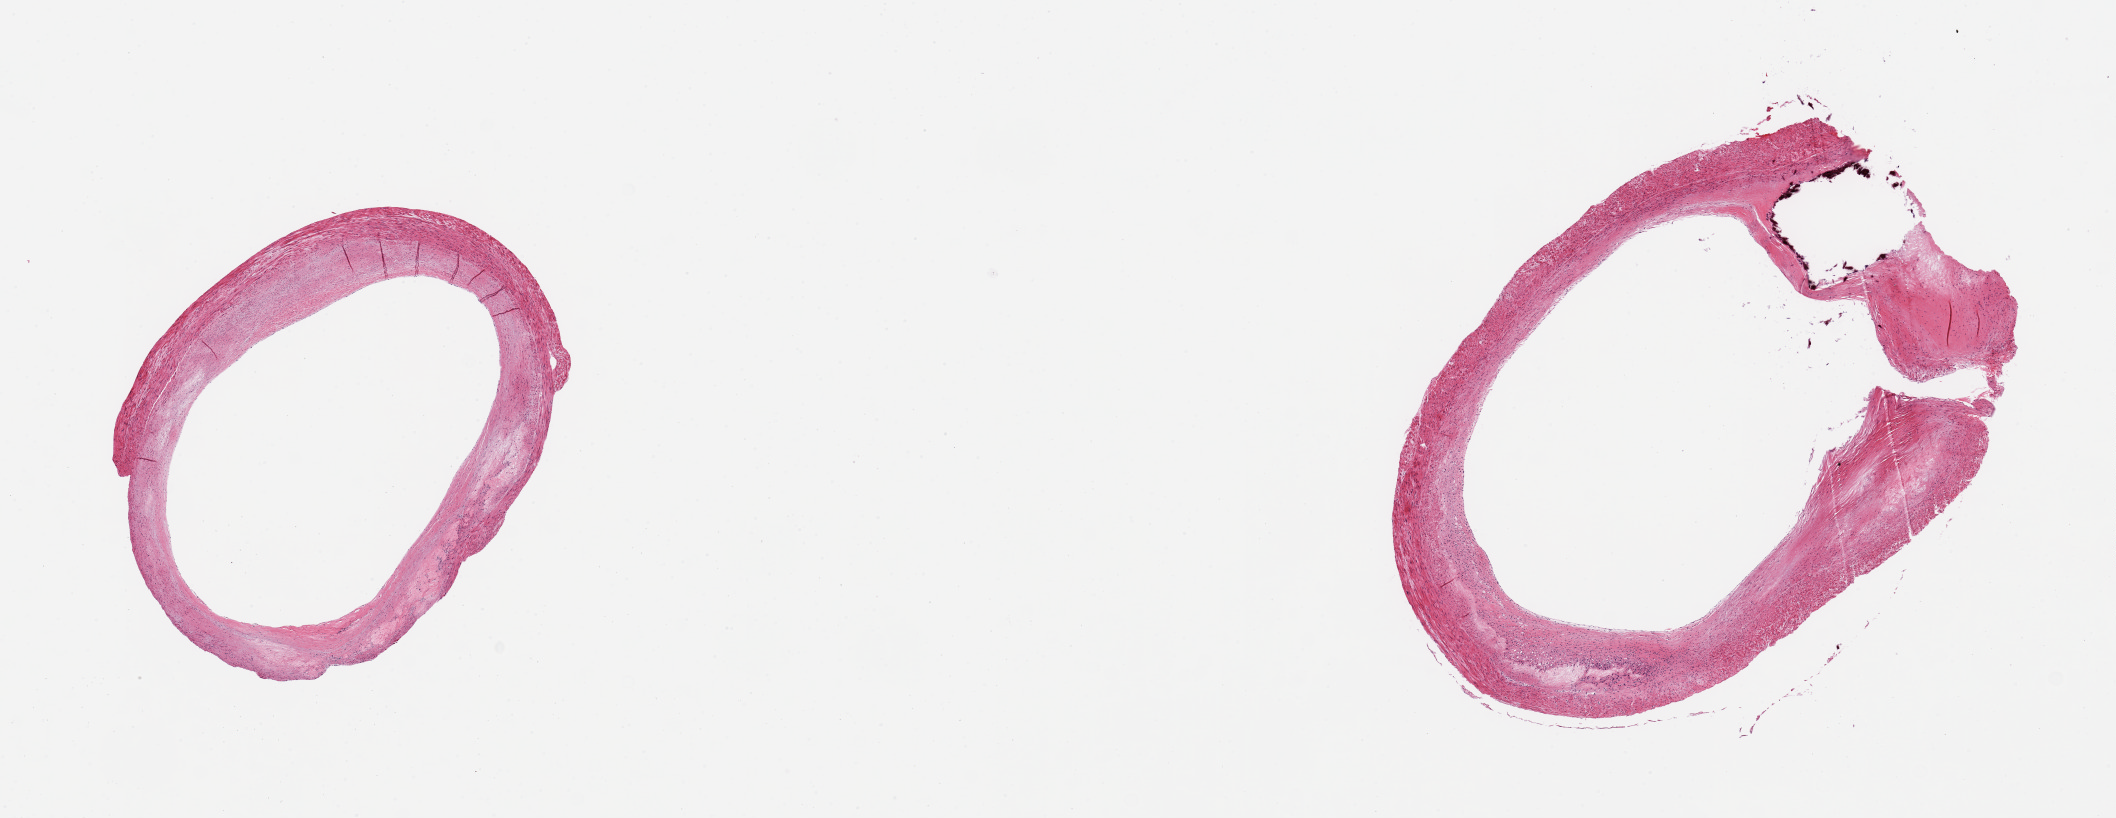
Digitized H&E-stained section, brightfield — whole scanned area (about 16.7 x 6.5 mm) shown as a low-resolution overview; PAXgene-fixed, paraffin-embedded tissue; sampled site (target tissue): coronary artery; tissue donor sample.
- review note (as recorded): 2 pieces, mild (20%) occlusive atherosis, focally calcified